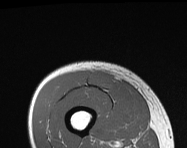
MRI of an extremity soft-tissue mass, one axial slice. MR volume resampled by the dataset authors to the PET/CT grid (not the native acquisition matrix). 3.27 mm slice thickness. 187 × 148 image matrix, field of view 183 × 145 mm. Male patient. Case-level facts recorded for this patient, not image findings: histological type: pleiomorphic leiomyosarcoma; grade: intermediate; site of the primary tumour: right thigh.
Annotated regions visible in this slice (expert contour drawn on MRI and transferred to this co-registered scan by the dataset authors):
- gross tumour volume including surrounding oedema: bounding box (x1, y1, x2, y2) in pixels: (88, 74, 112, 89)